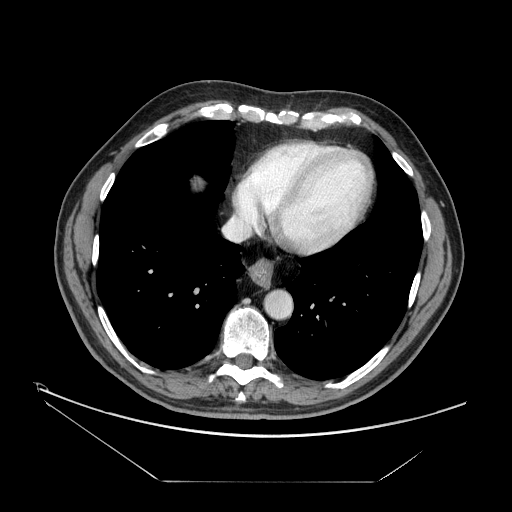
Contrast-enhanced abdominal CT, one axial slice. Slice 156 of 161 in the series (ordered by position). Reconstruction kernel STANDARD. Intravenous contrast given. Soft-tissue window (W 400 / L 40 HU). 2.5 mm slice thickness. 512 × 512 image matrix. Male patient, age 65 years. From the clinical record (not read from this slice): diagnosis: colorectal cancer liver metastases, imaged before liver resection; multiple liver metastases: yes; largest metastasis: 4.2 cm; disease in both lobes: yes.
Annotated regions visible in this slice (manually delineated by an expert):
- hepatic veins: bounding box <223,161,266,241> (left, top, right, bottom; pixels)